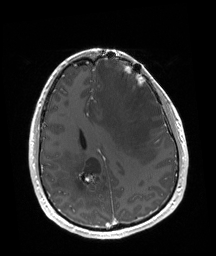
Brain MRI from a brain-tumour surgery series, one axial slice. Position 65 of 192 along the scan axis. T1-weighted post-contrast. 1 mm slice thickness. 216 × 256 image matrix, field of view 219 × 260 mm. Case-level facts recorded for this patient, not image findings: tumour location: Left Frontal.
Structures marked on this image (manually delineated by an expert):
- tumour: bounding box [x1, y1, x2, y2] px = [122, 66, 145, 88]